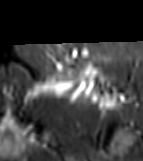
MRI of an extremity soft-tissue mass, one axial slice. Slice 49 of 81 in the series (ordered by position). STIR. MR volume resampled by the dataset authors to the PET/CT grid (not the native acquisition matrix). 143 × 161 image matrix, field of view 140 × 157 mm. Female patient. Case-level facts recorded for this patient, not image findings: histological type: myxofibrosarcoma; grade: intermediate; site of the primary tumour: left thigh.
Outlined on this slice (expert contour drawn on MRI and transferred to this co-registered scan by the dataset authors):
- gross tumour volume including surrounding oedema: bounding box [x1, y1, x2, y2] px = [26, 65, 119, 107]